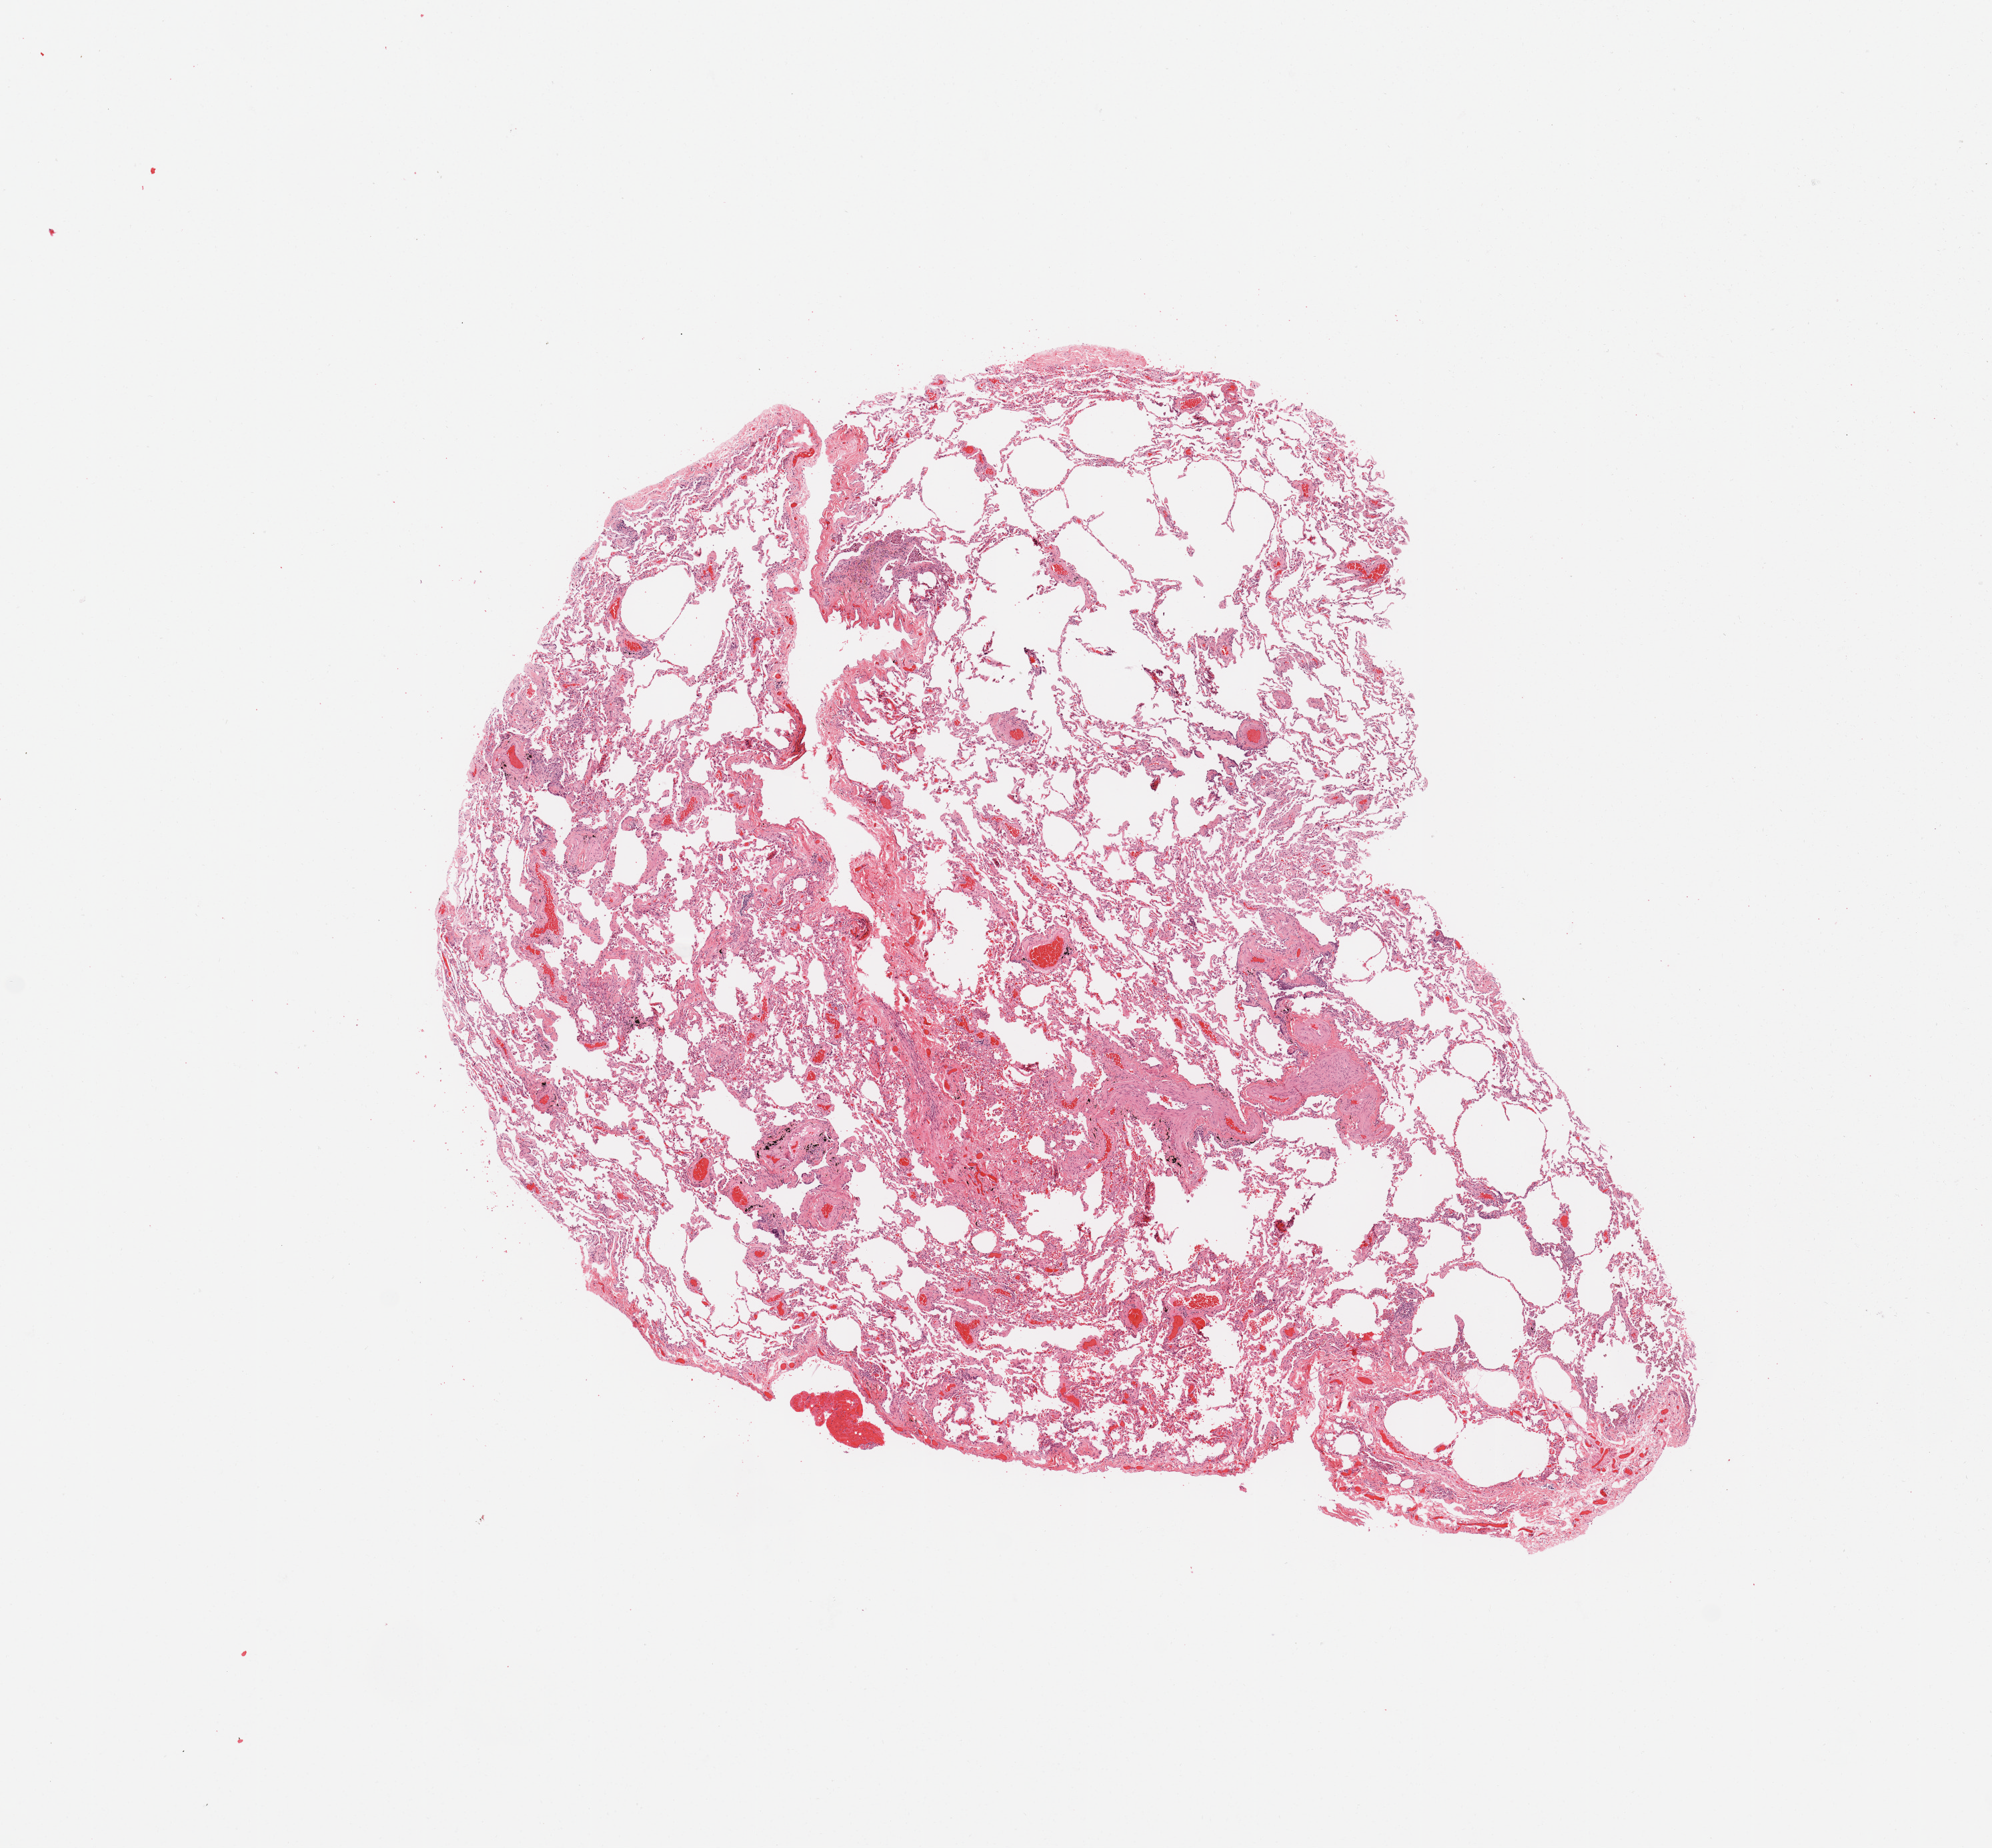
Digitized H&E tissue section (whole slide) — a low-resolution overview of the entire scanned area, about 11.8 x 11.0 mm (acquisition: 20x scan); normal (non-tumour) tissue sample, sampled site: lung. Male, 73 y/o.
This section: normal (non-tumour) tissue from the same patient. Patient diagnosis: Adenocarcinoma, NOS.